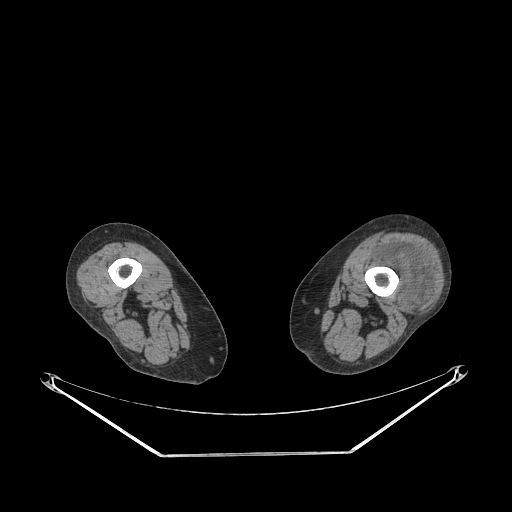
CT of an extremity soft-tissue mass (from a PET/CT study), one axial slice. Position 200 of 267 along the scan axis. 140 kVp. Soft-tissue window (W 400 / L 40 HU). 512 × 512 image matrix. Female patient. Case-level facts recorded for this patient, not image findings: histological type: undifferentiated – high grade; grade: high; site of the primary tumour: left thigh.
Structures marked on this image (expert contour drawn on MRI and transferred to this co-registered scan by the dataset authors):
- gross tumour volume including surrounding oedema: bounding box (x1, y1, x2, y2) in pixels: (372, 246, 433, 307)